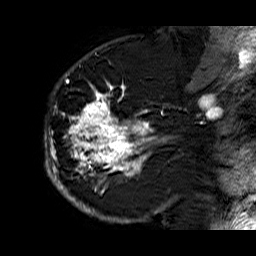
Breast MRI (dynamic contrast-enhanced), one sagittal slice. Slice 41 of 60 in the series (ordered by position). Dynamic contrast-enhanced series, time point 2 of 6 at this slice position (early post-contrast). 1.5 T. TE 6.3 ms, TR 32.9 ms. 4 mm slice thickness. 256 × 256 image matrix. Female patient. Case-level facts recorded for this patient, not image findings: setting: breast cancer imaged before/during neoadjuvant chemotherapy; receptor status: HR-positive, HER2-negative.
Outlined on this slice (semi-automatically segmented with operator editing):
- analysis volume of interest (the breast-tissue region the enhancement analysis was run in; not a lesion): box from (x=44, y=74) to (x=176, y=210) px
- tumour enhancement mask (voxels above the 100 % enhancement threshold inside the analysis volume of interest): (x=45, y=74)–(x=169, y=210)